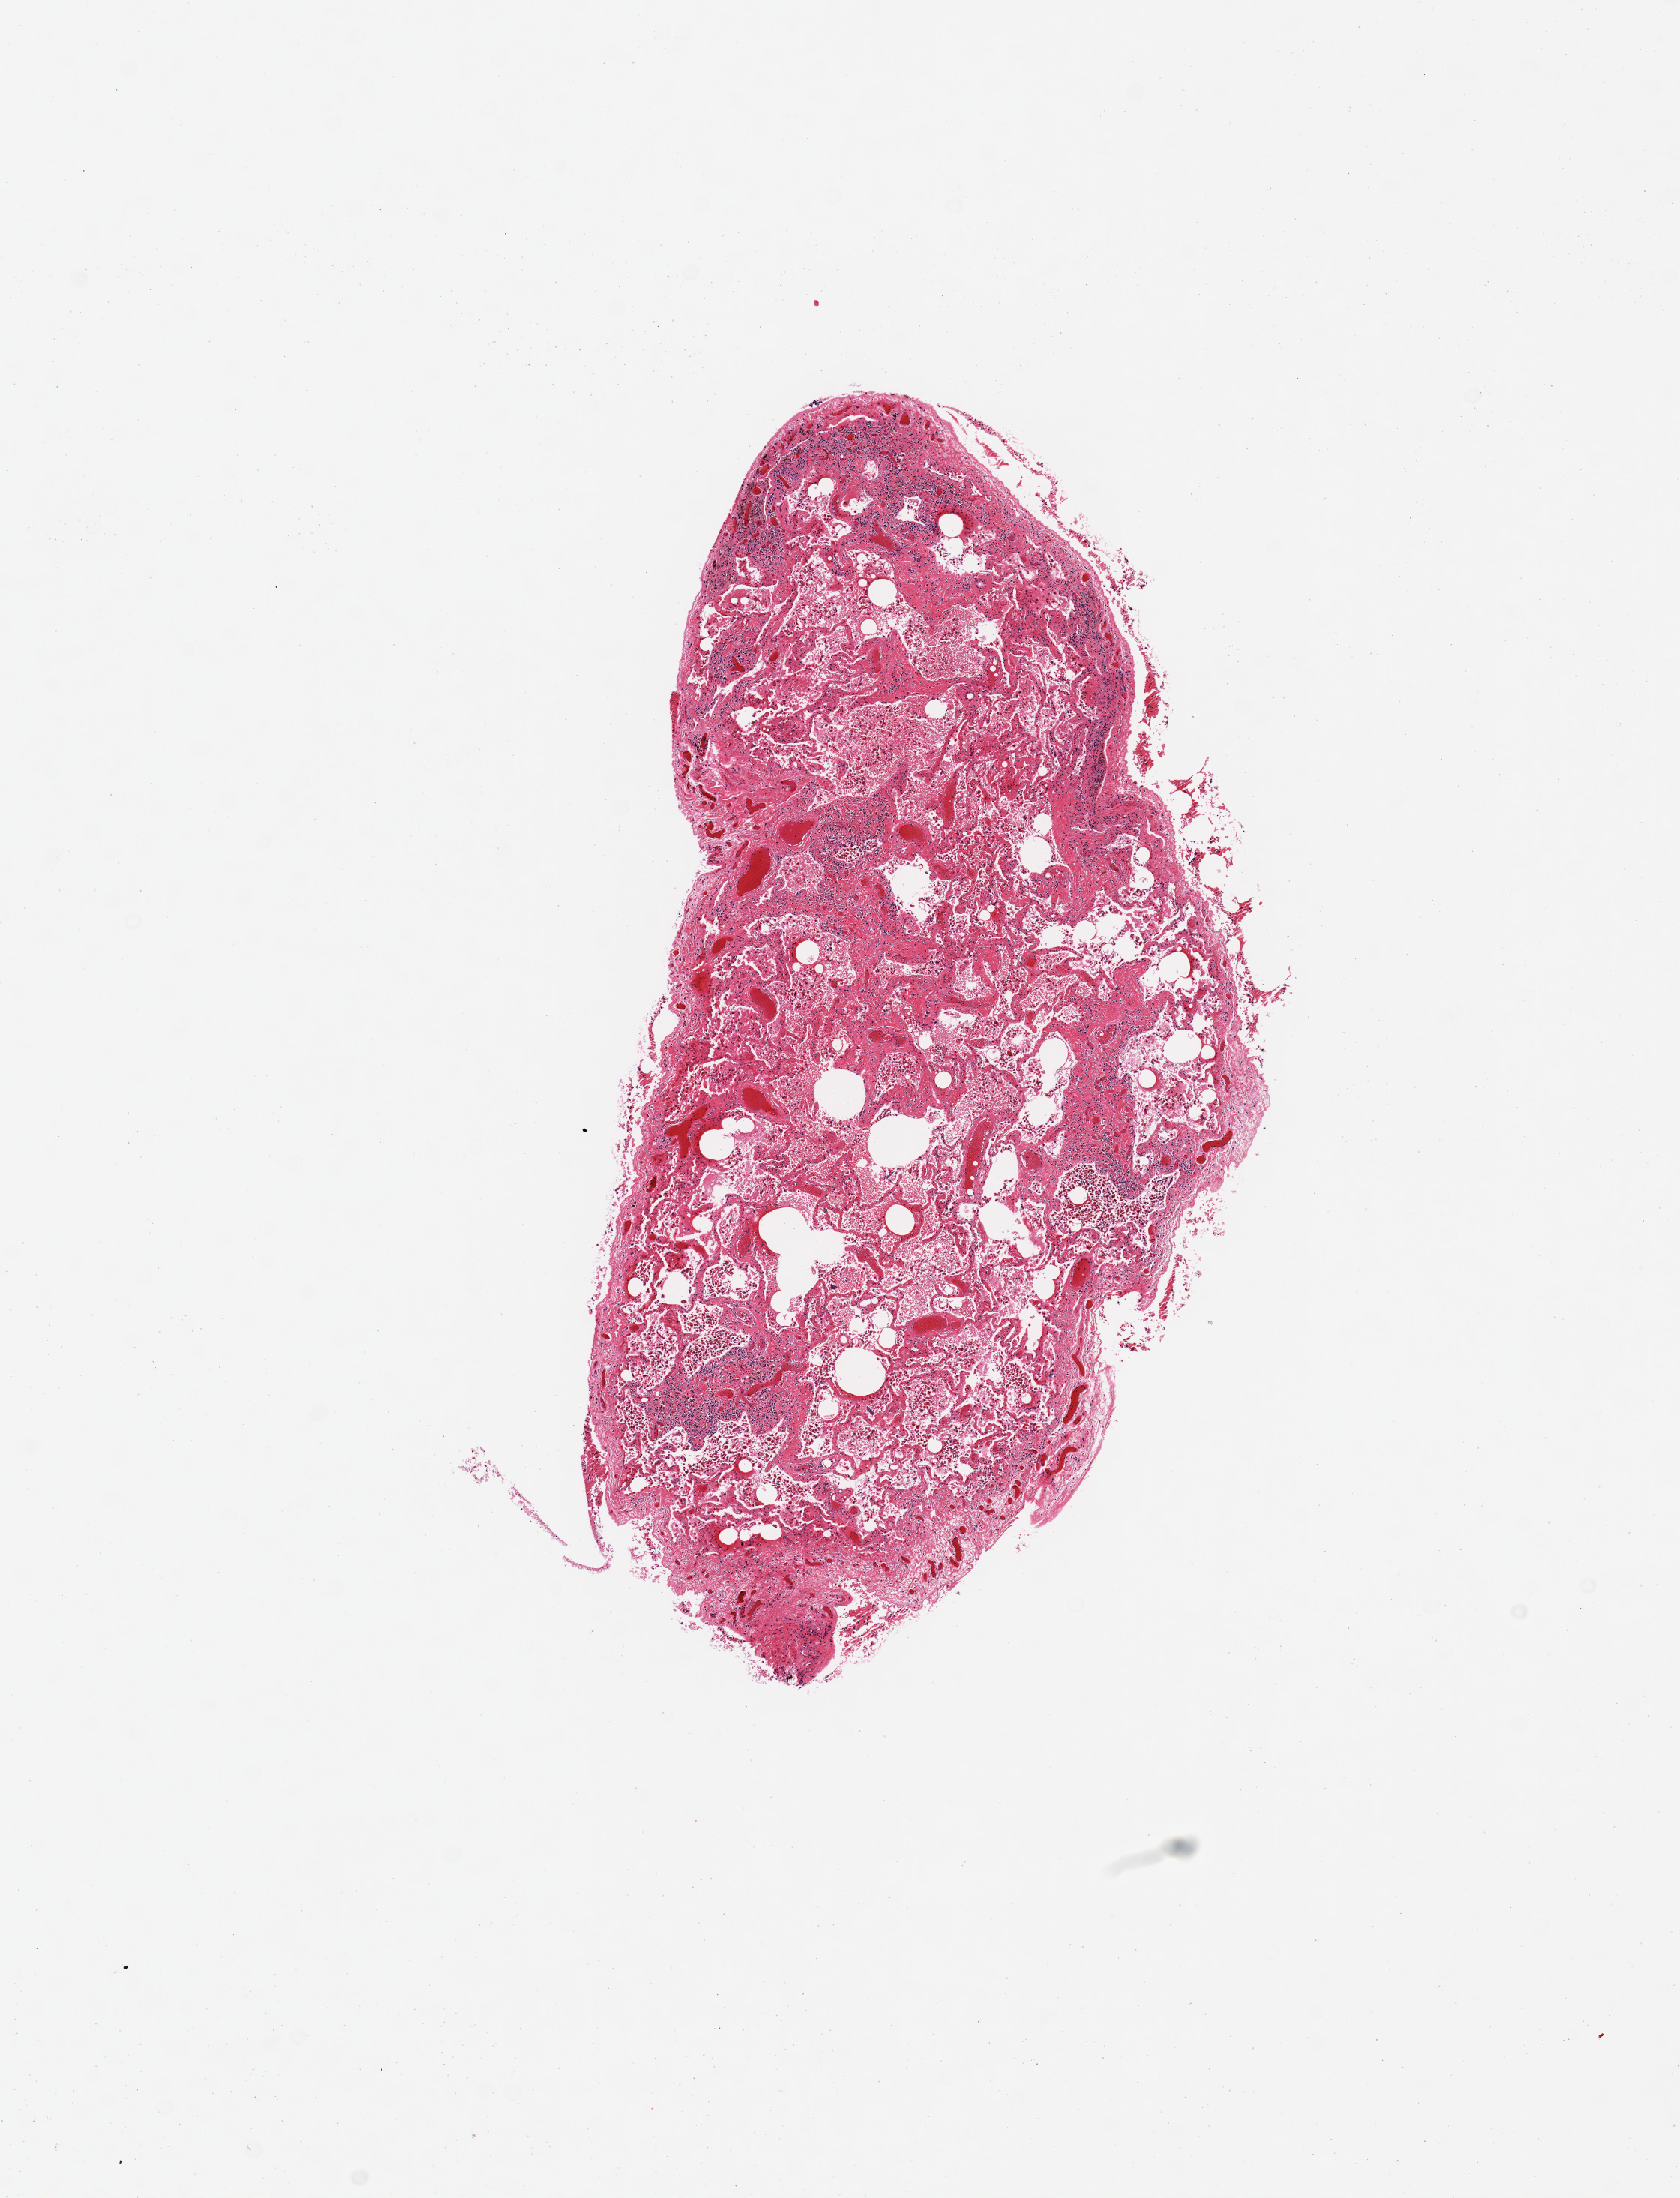
H&E whole-slide image, brightfield — low-resolution overview of the scanned area, about 8.9 x 11.6 mm (from a 20x scan); PAXgene-fixed, paraffin-embedded tissue; target tissue: lung; donor tissue sample.
Reviewer comment on this tissue sample: 1 piece; pronounced edema; moderate-marked septal fibrosis.